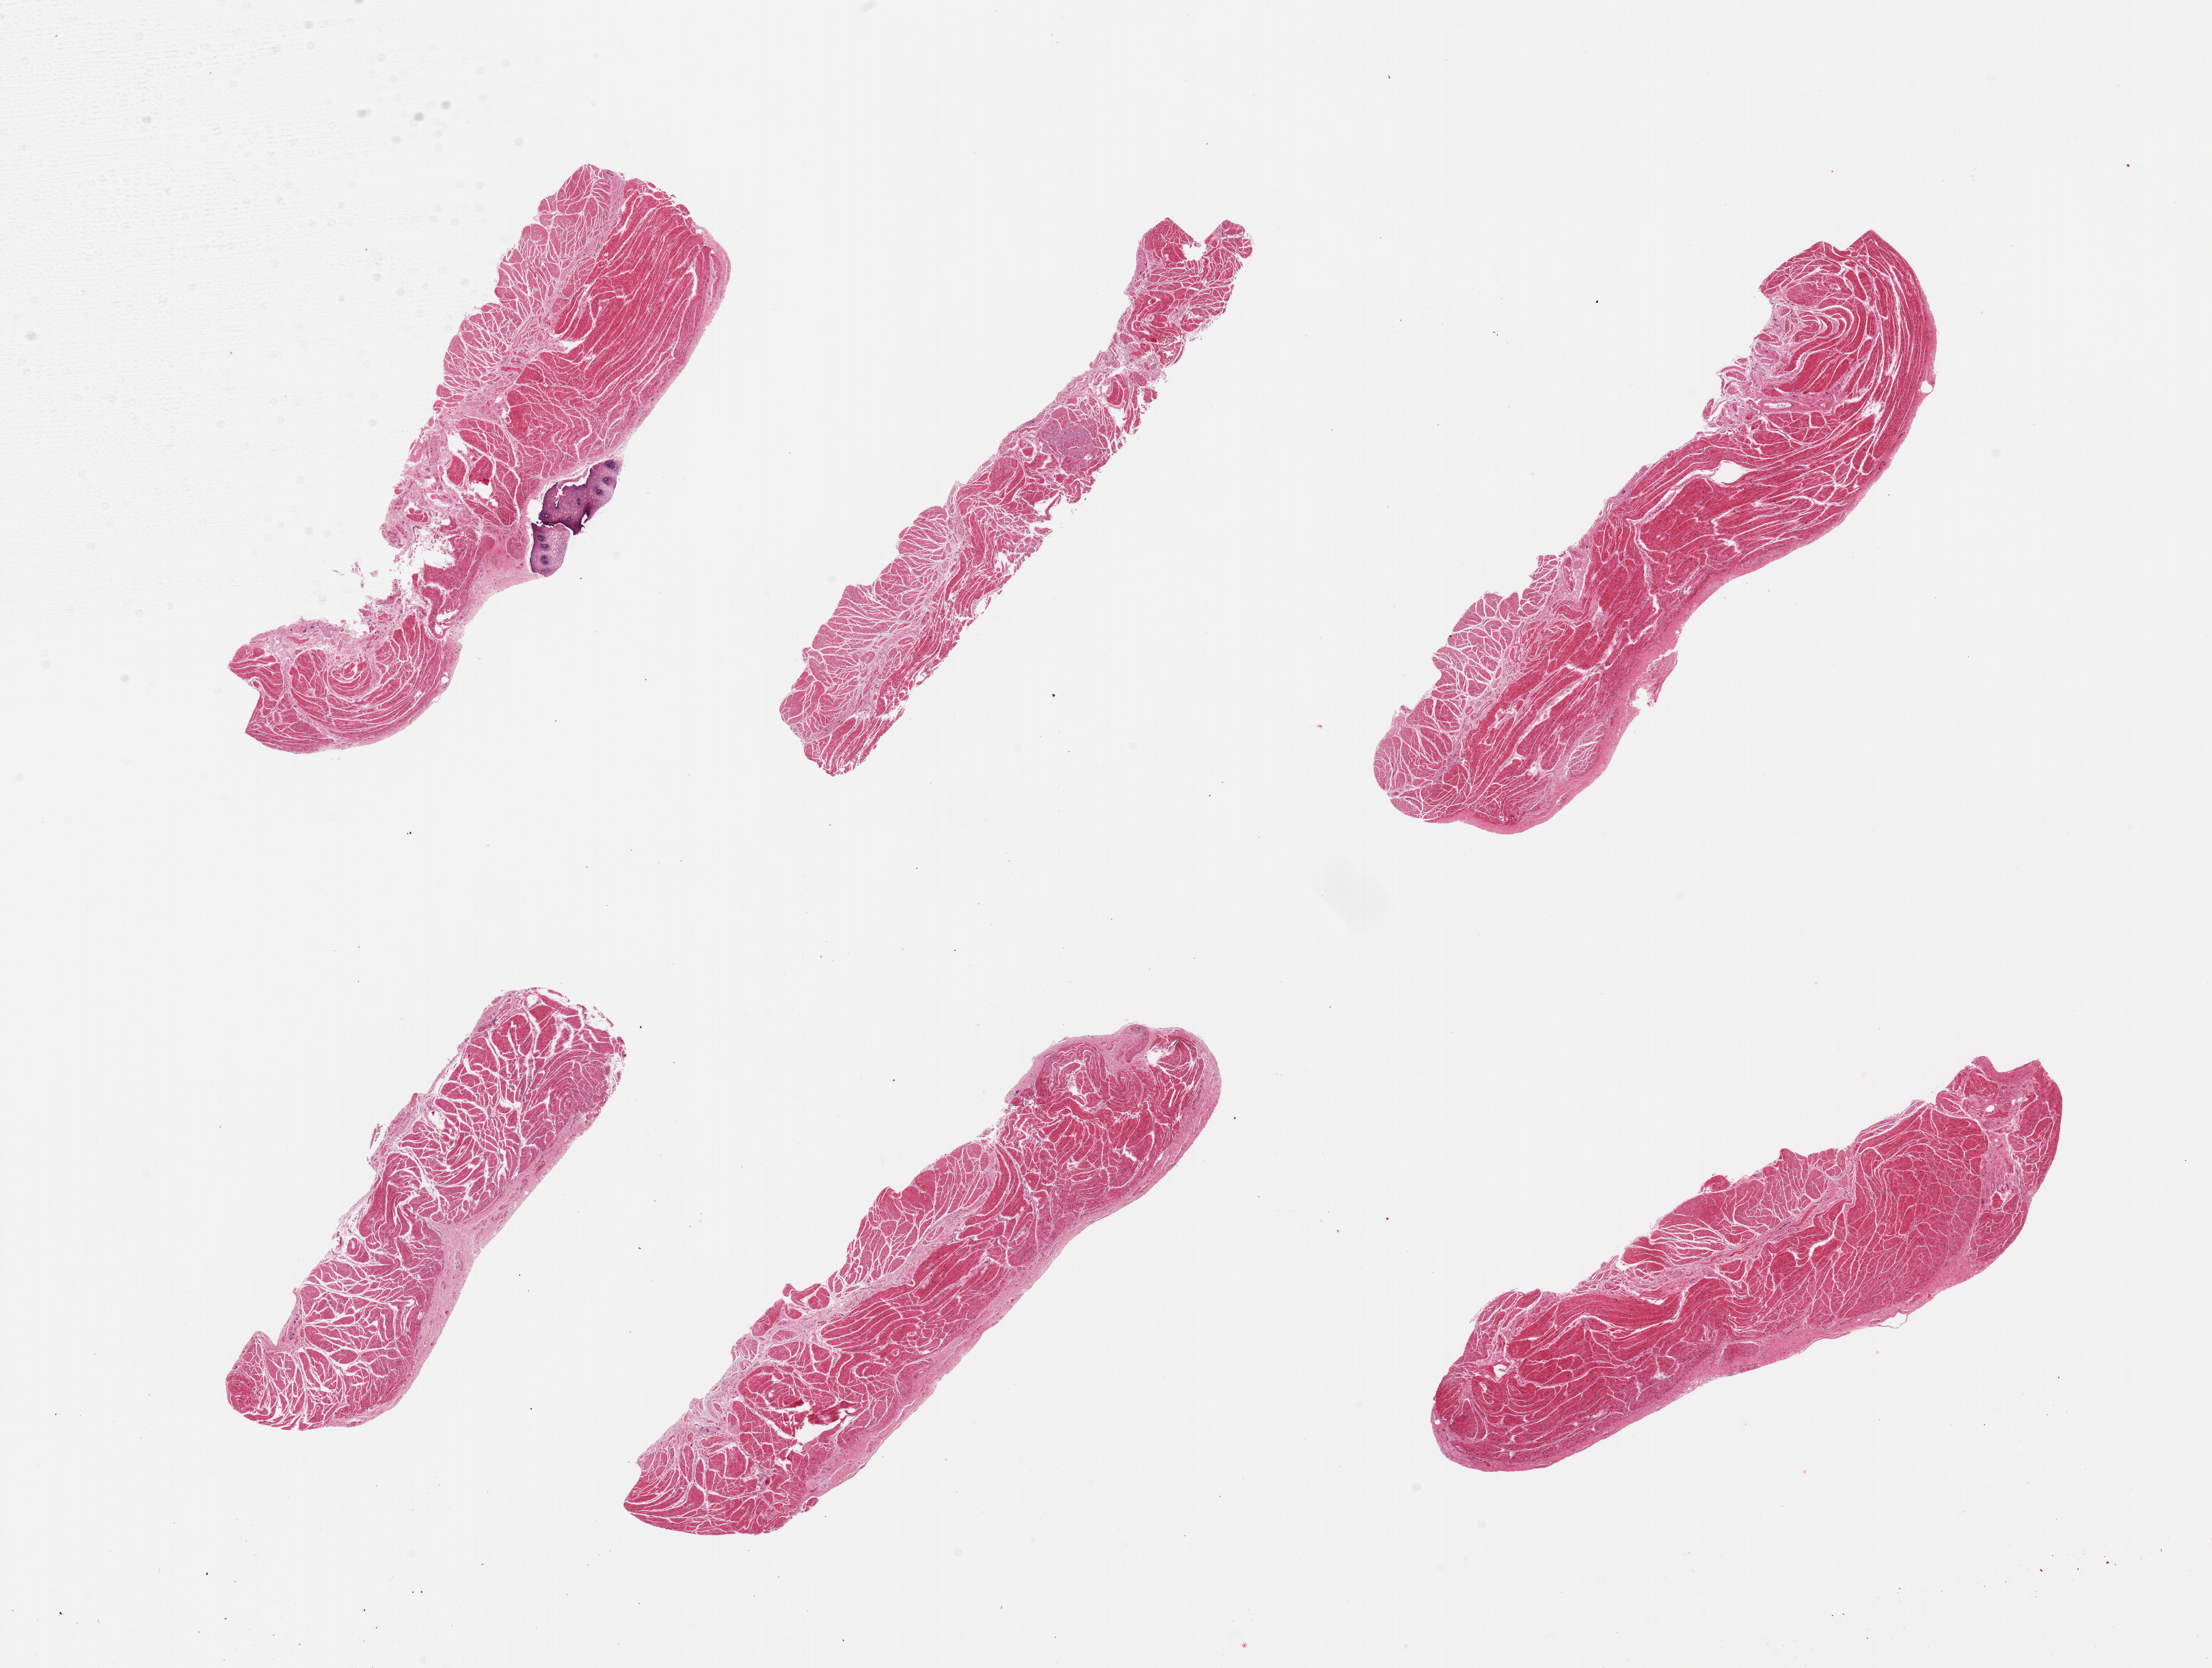
Whole-slide image, hematoxylin and eosin (H&E) stain, shown as a low-resolution overview of the whole scanned area (about 25.6 x 19.3 mm, from a 20x scan), PAXgene-fixed, paraffin-embedded tissue, target tissue: esophageal muscle, tissue donor sample. Donor sex: female.
- review note (as recorded): 6 pieces; small residual fragment of squamous epithelium